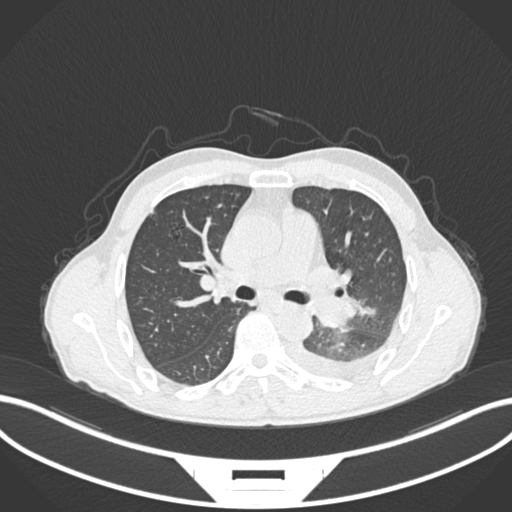
Chest CT, one axial slice. Position 152 of 222 along the scan axis. Reconstruction kernel B30f. 120 kVp. Lung window (W 1500 / L -600 HU). 1 mm slice thickness. 512 × 512 image matrix, field of view 400 × 400 mm. Patient: male, 47 years. Case-level facts recorded for this patient, not image findings: clinical TNM (as recorded): T3 N1 M1c; histopathological grade: G3.
Structures marked on this image (rectangle marked by the reading radiologist):
- lung tumour (recorded histology: small cell carcinoma): box from (x=311, y=293) to (x=359, y=330) px